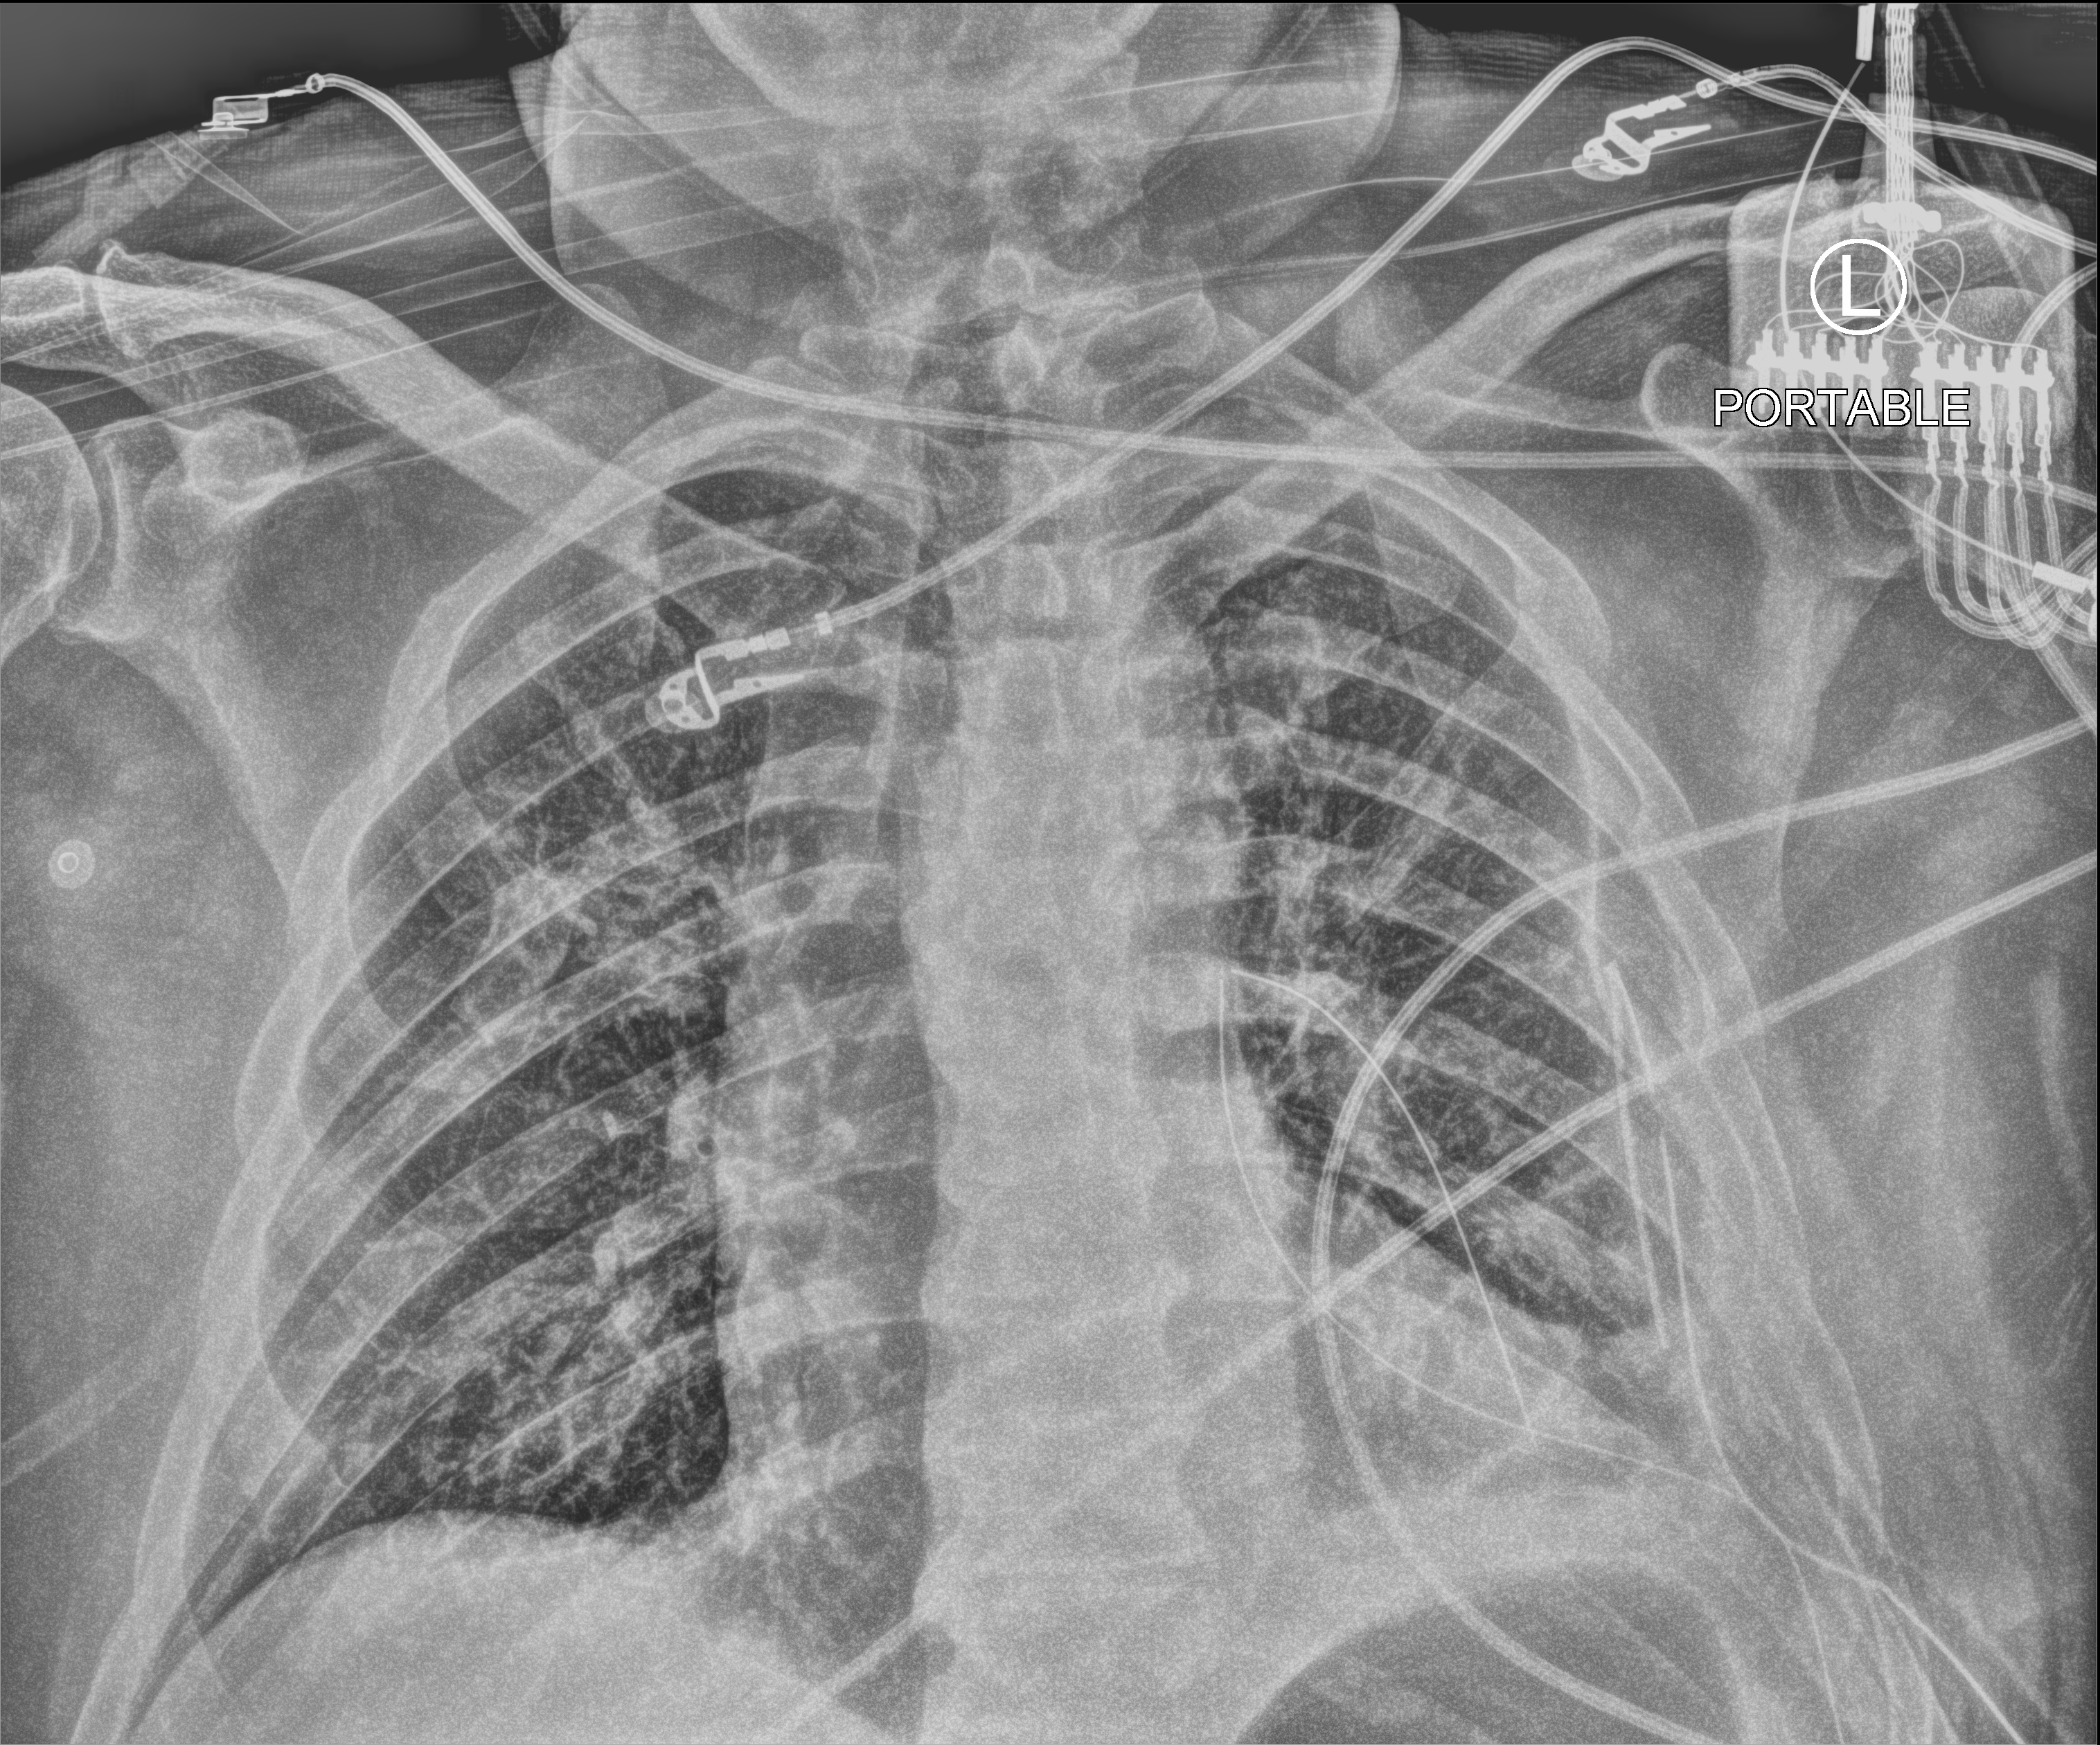
Chest X-ray (portable); anteroposterior (AP) projection. Patient hospitalised with COVID-19; male, aged 18–59 years.
Hospital-stay facts (about this admission, not read from this image; timing relative to this image not recorded):
- mechanically ventilated during this hospital stay: no